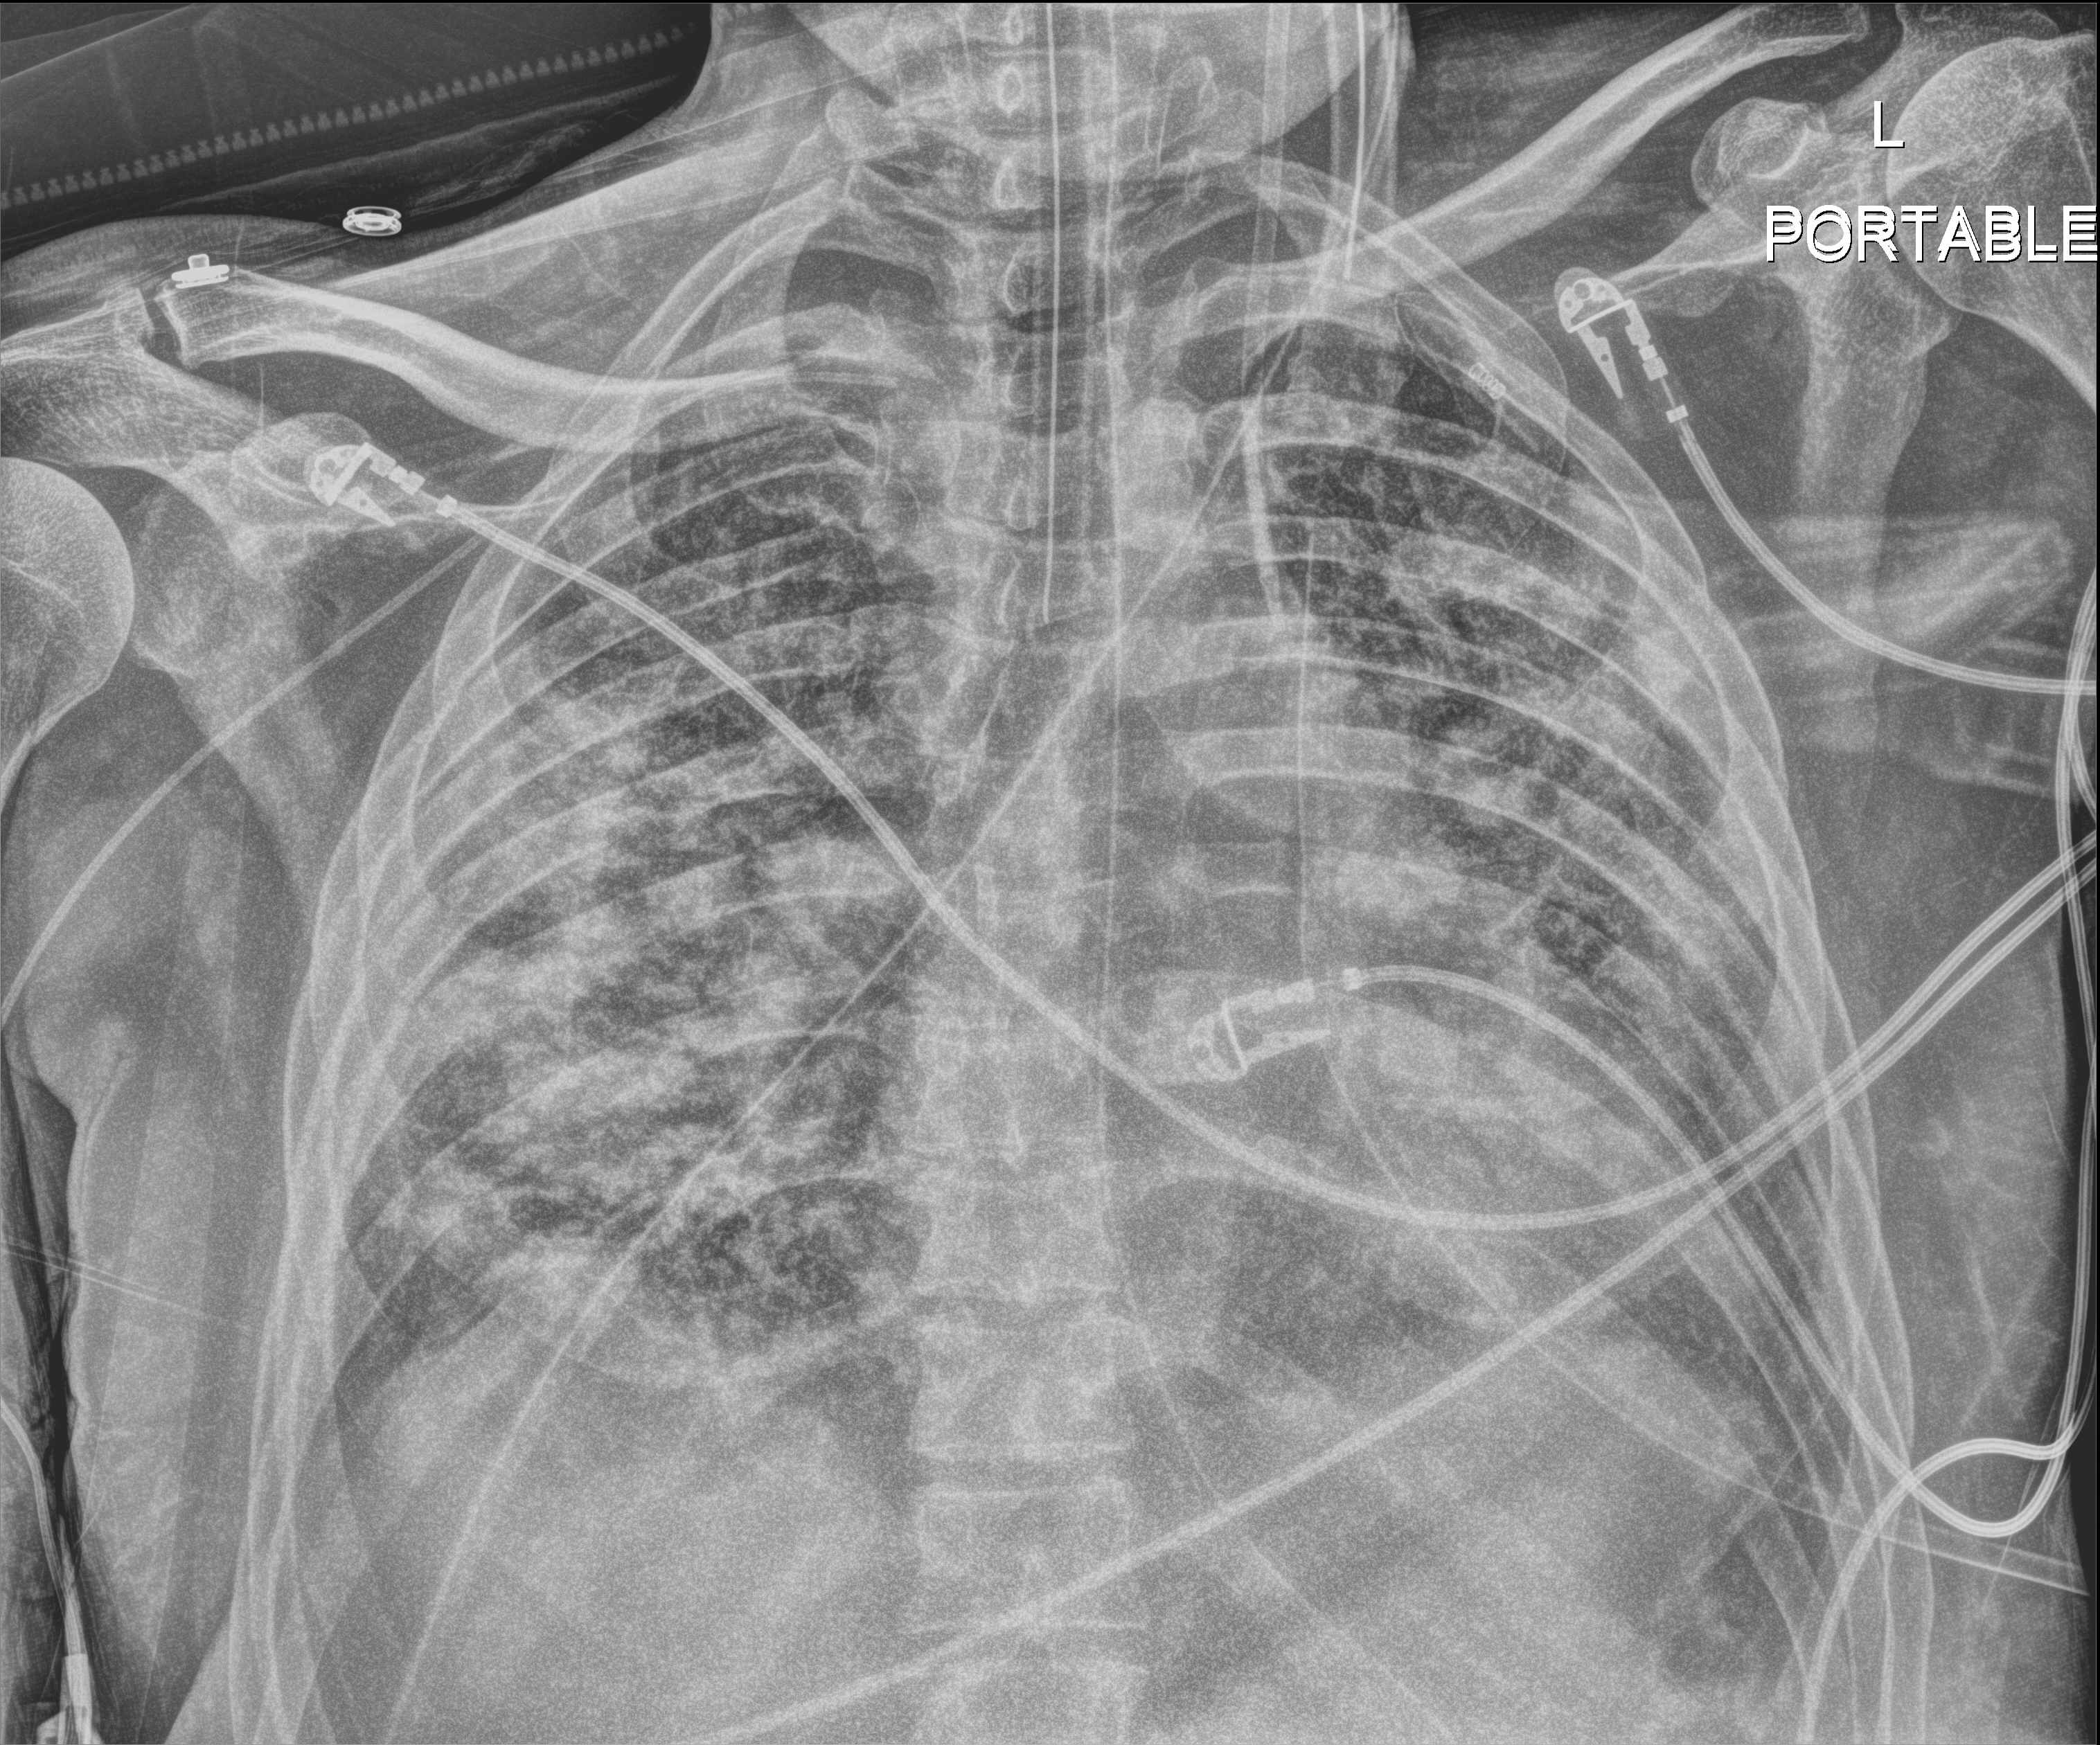
Chest X-ray; anteroposterior (AP) projection. Male patient hospitalised with COVID-19, age 18–59 years.
Hospital-stay facts (about this admission, not read from this image; timing relative to this image not recorded): admitted to intensive care during this hospital stay: yes; mechanically ventilated during this hospital stay: yes.